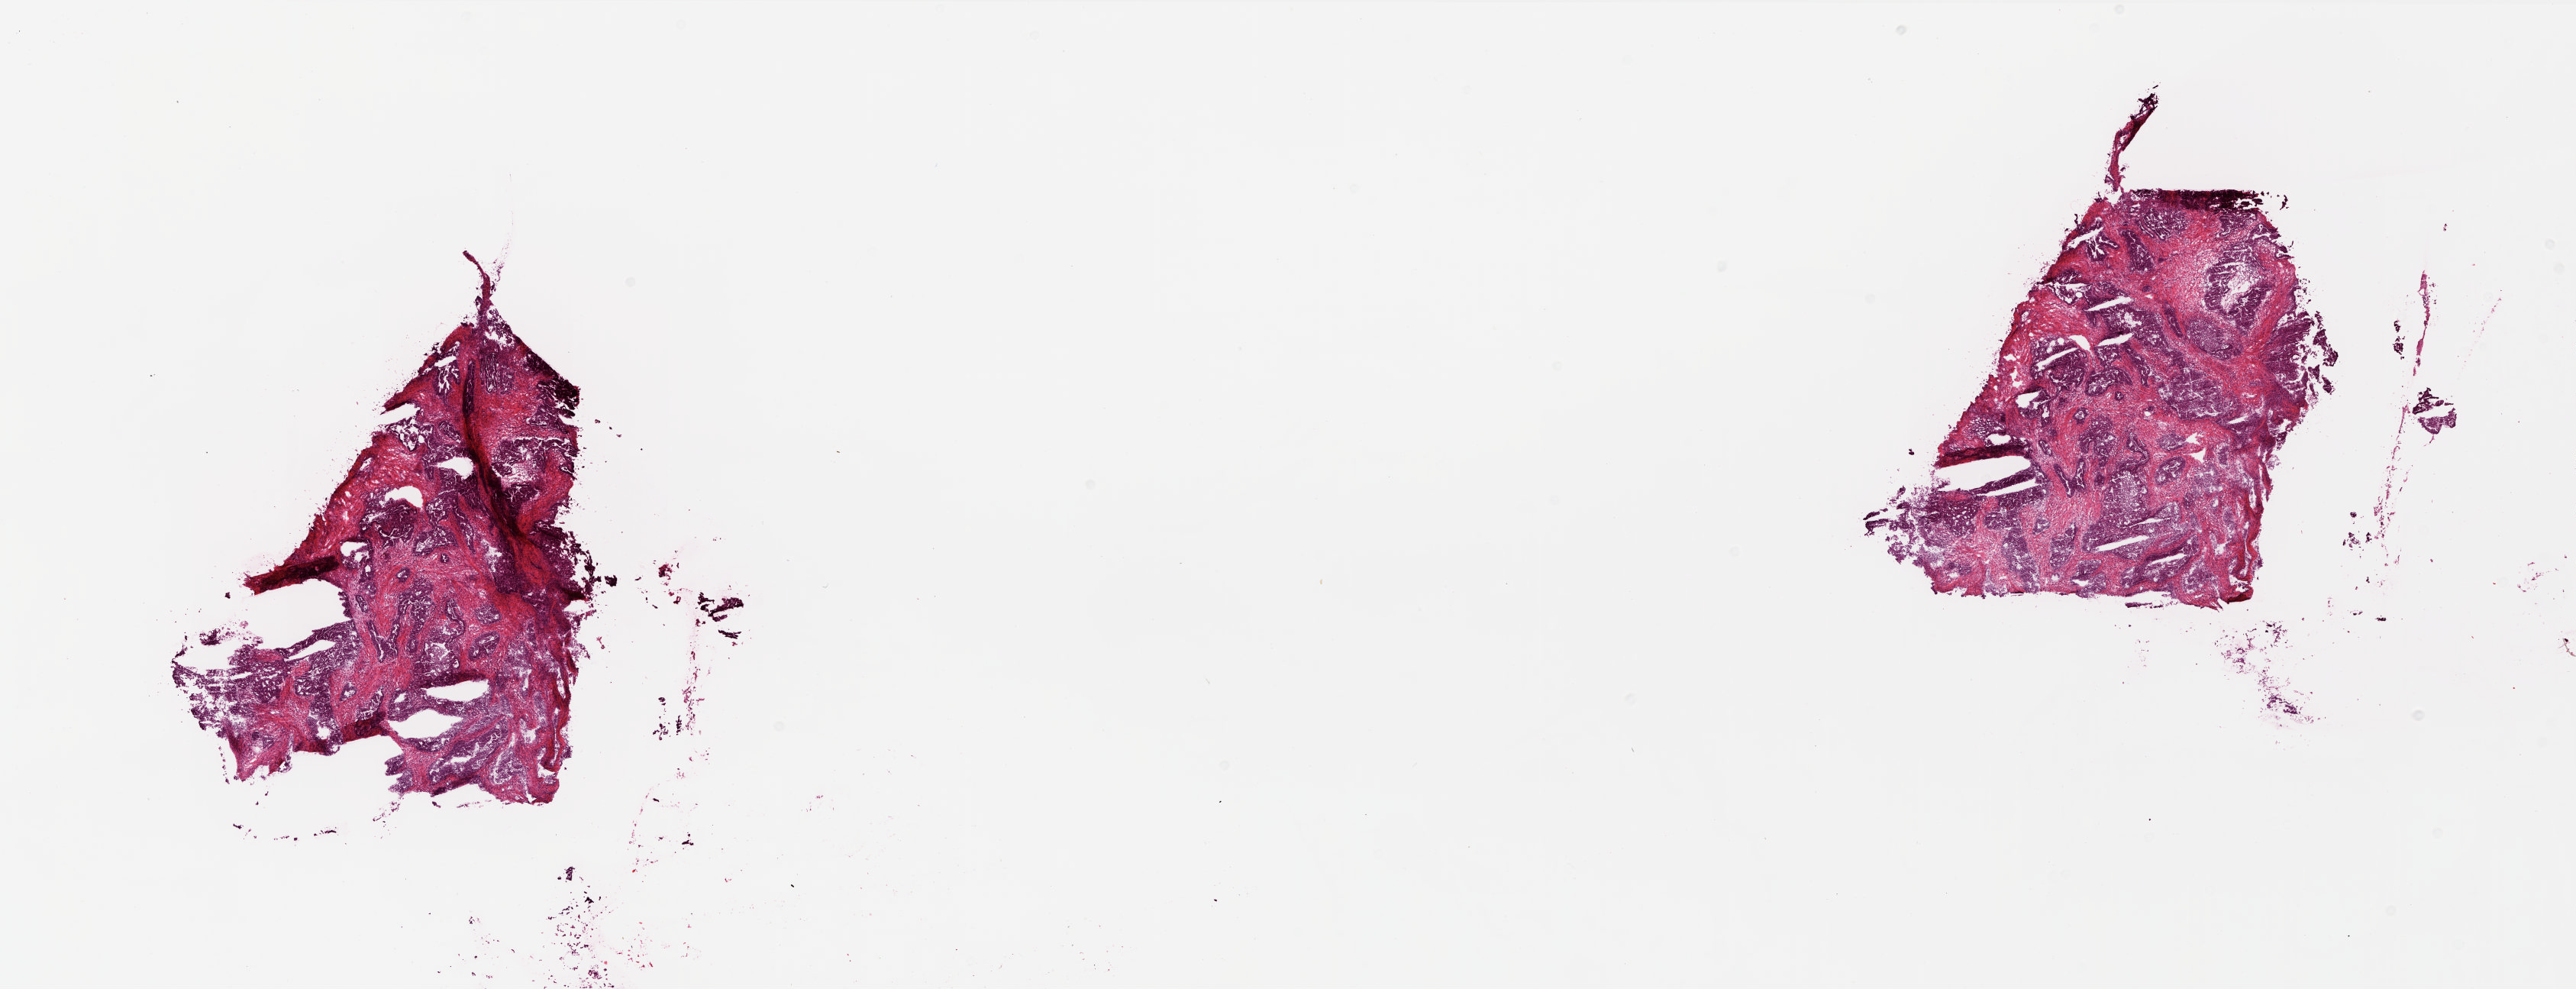
Digitized Hematoxylin and eosin (H&E) stained tissue section (whole slide), a low-resolution overview of the entire scanned area, about 26.9 x 10.3 mm (from a 20x scan), frozen section from the top of the tissue portion, ovary, primary tumour sample. Female, age 73 years at initial diagnosis. Histologic grade: G2 (moderately differentiated). Pathologist review of this section (percent, as recorded): tumour cells 68%, tumour nuclei 90%, normal cells 0%, stromal cells 30%, necrosis 2%.
Pathologic diagnosis: Serous cystadenocarcinoma, NOS. Laterality: bilateral. FIGO stage: IIIC.